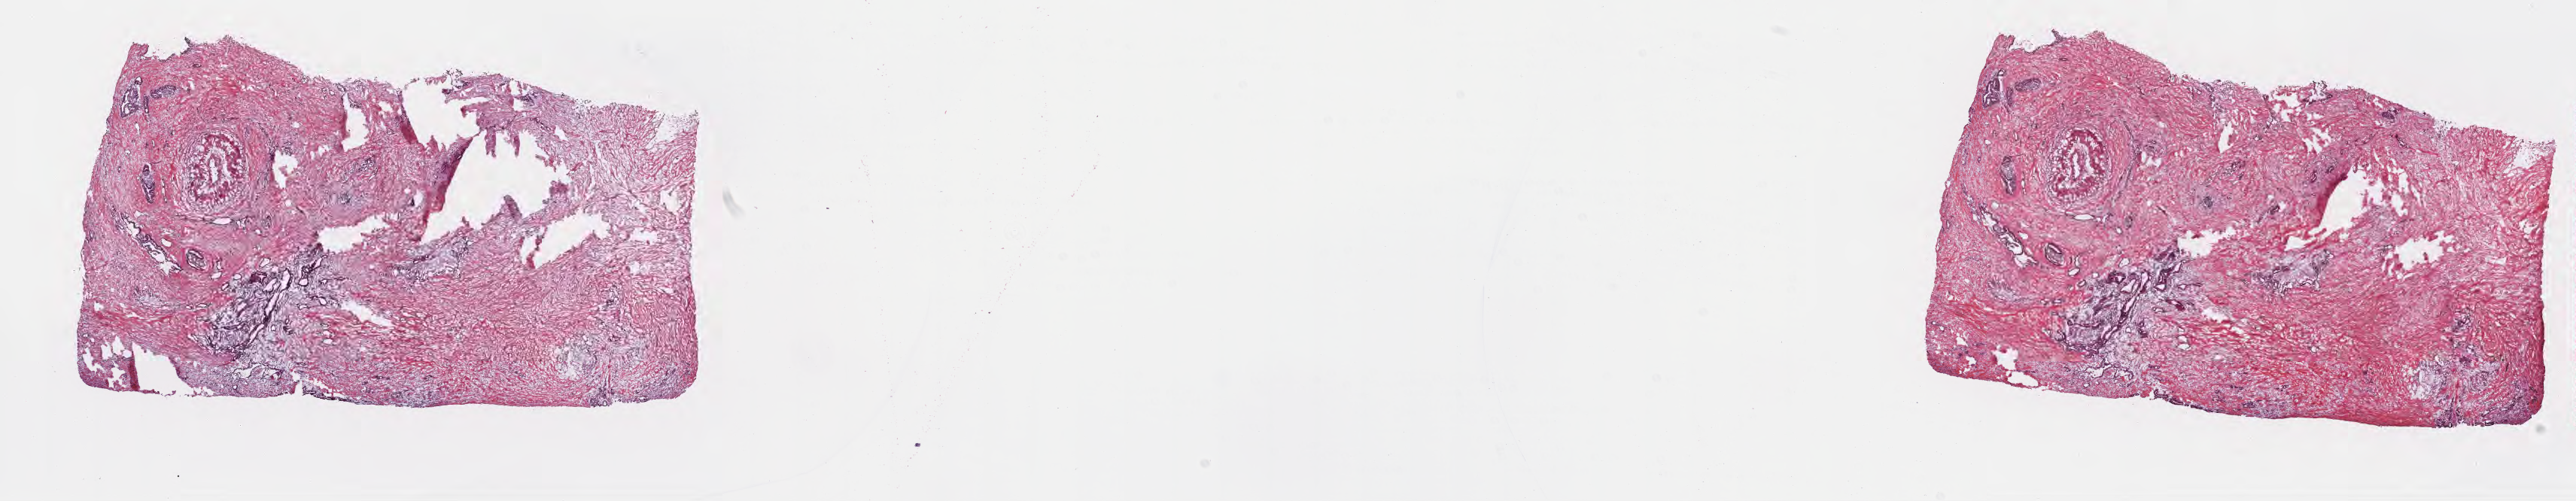
Haematoxylin and eosin whole-slide image — shown as a low-resolution overview of the whole scanned area (about 27.7 x 5.4 mm), cryosection, primary tumor, site: tail of pancreas. Male, age 39 years at initial diagnosis. Pathologist review of this section (percent, as recorded): tumor cells 9%, tumor nuclei 35%, stromal cells 90%, necrosis 1%, normal cells 0%. Inflammatory infiltration, as recorded: lymphocyte infiltration 5%, monocyte infiltration 1%, neutrophil infiltration 0%.
• section: top of the tissue portion
• histologic diagnosis: Infiltrating duct carcinoma, NOS